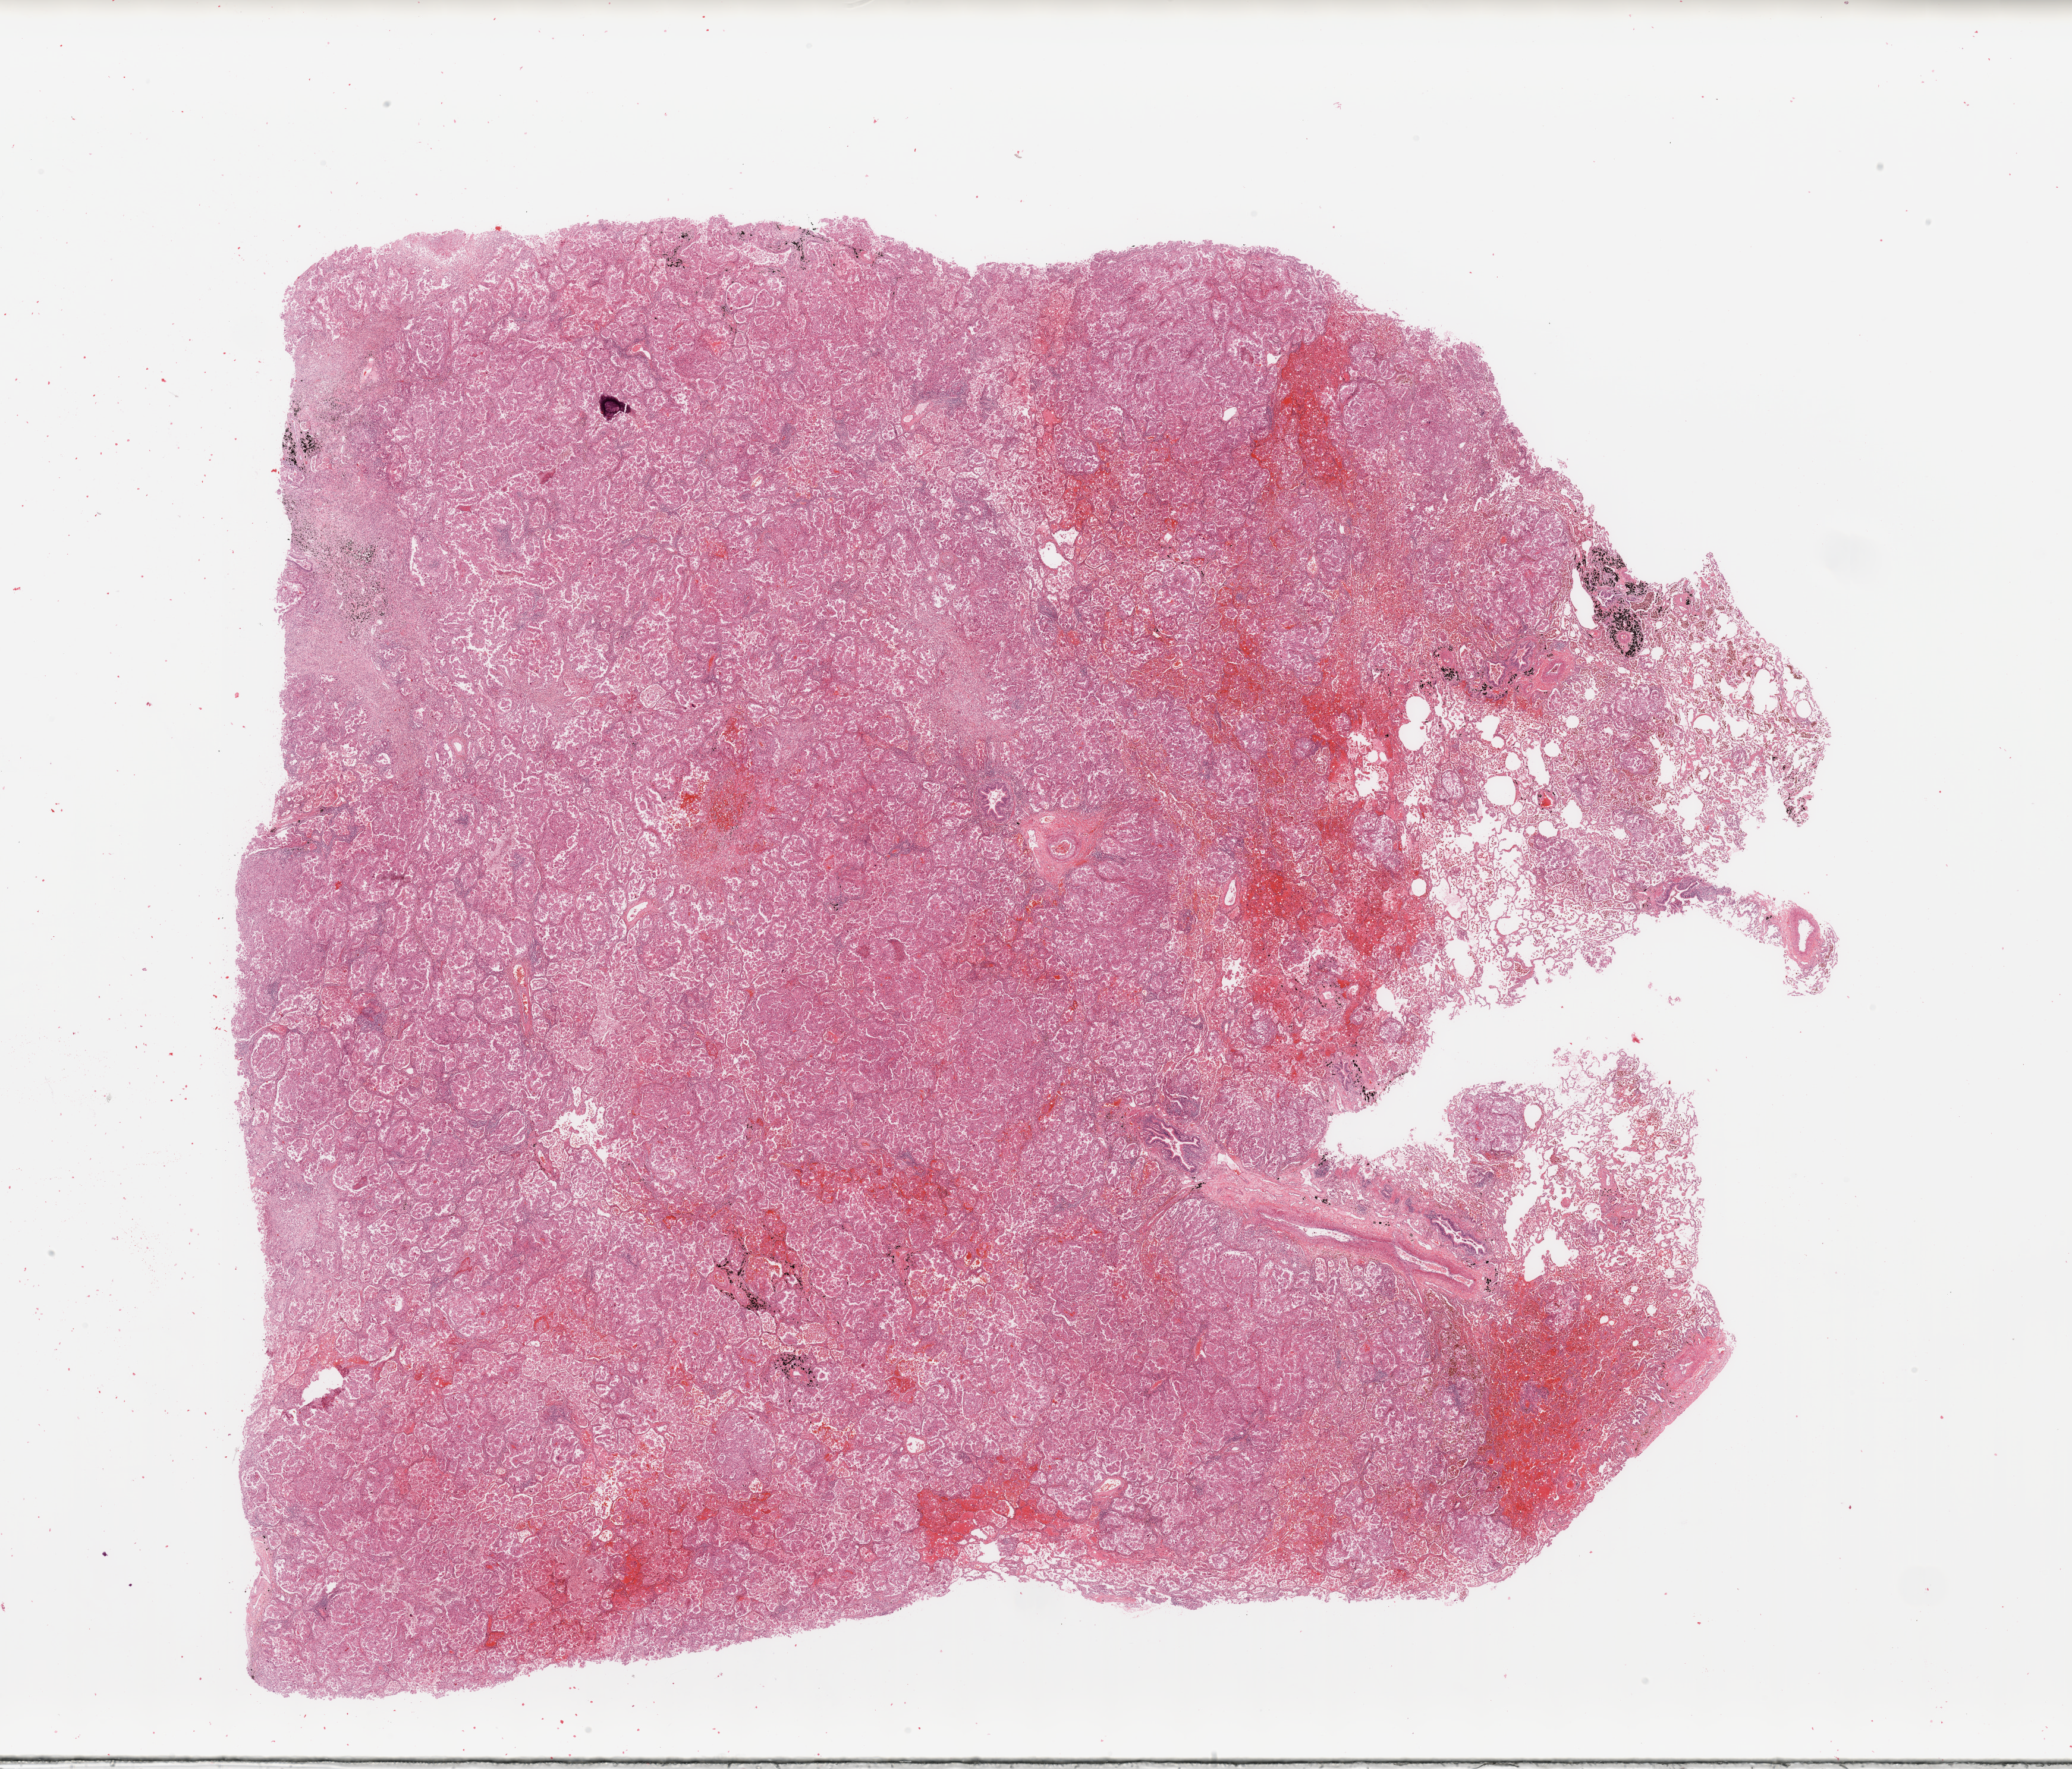
Hematoxylin and eosin (H&E) stained whole-slide image — a low-resolution overview of the entire scanned area, about 27.6 x 23.5 mm (acquisition: 20x scan). Tumour tissue sample, sampled site: lung. Male, 55 y/o. Histologic grade: G2 (moderately differentiated). Pathologist review of this section (percent, as recorded): tumour nuclei 75%, necrosis 5%.
Histologic diagnosis: Adenocarcinoma, NOS. AJCC pathologic stage: IIIA.